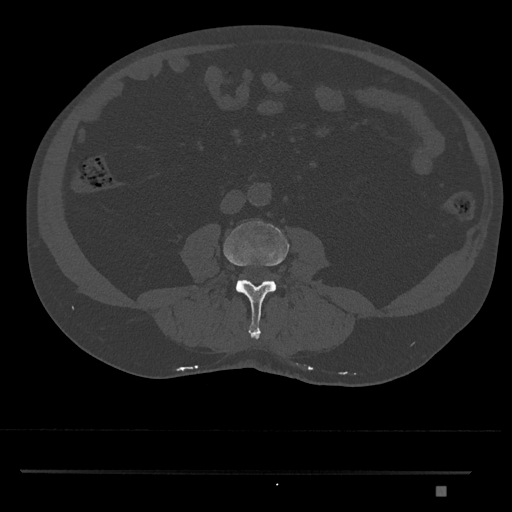
CT including the spine, one axial slice; slice 668 of 1134 in the series (ordered by position); 120 kVp; bone window (W 1800 / L 400 HU); 0.5 mm slice thickness; 512 × 512 image matrix, field of view 429 × 429 mm. Patient: male, 65 years. Case-level facts recorded for this patient, not image findings: primary cancer: prostate.
Annotated regions visible in this slice (semi-automatic segmentation, software-assisted and operator-edited):
- L3 vertebra: bounding box [x1, y1, x2, y2] px = [223, 221, 289, 340]